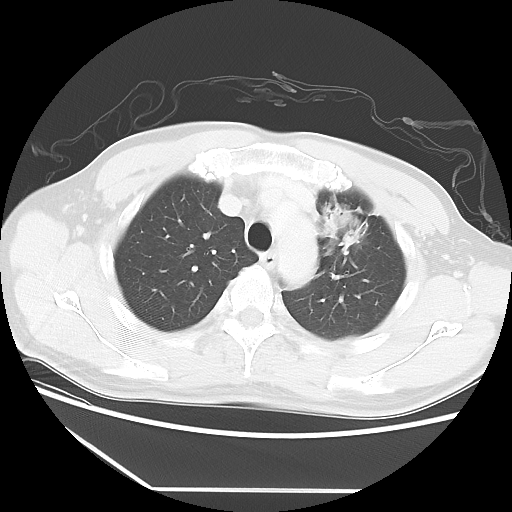
Chest CT, one axial slice. Position 43 of 56 along the scan axis. Reconstruction kernel LUNG. Lung window (W 1500 / L -600 HU). 512 × 512 image matrix. Patient: male, 53 years. Case-level facts recorded for this patient, not image findings: clinical TNM (as recorded): T2a N1 M1b.
Outlined on this slice (rectangle marked by the reading radiologist):
- lung tumour (recorded histology: adenocarcinoma): box from (x=321, y=201) to (x=372, y=254) px